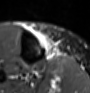
MRI of an extremity soft-tissue mass, one axial slice. Slice 19 of 60 in the series (ordered by position). STIR. MR volume resampled by the dataset authors to the PET/CT grid (not the native acquisition matrix). 90 × 93 image matrix, field of view 88 × 91 mm. Female patient. Case-level facts recorded for this patient, not image findings: histological type: undifferentiated – high grade; grade: high; site of the primary tumour: right thigh.
Structures marked on this image (expert contour drawn on MRI and transferred to this co-registered scan by the dataset authors):
- gross tumour volume (mass): bounding box <35,30,59,56> (left, top, right, bottom; pixels)